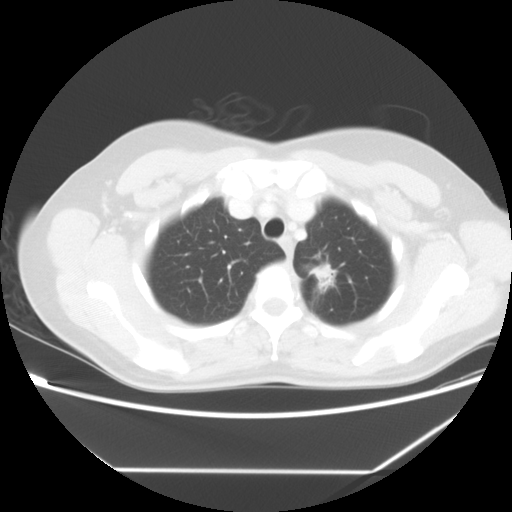
Chest CT, one axial slice. Position 49 of 60 along the scan axis. Reconstruction kernel STANDARD. Lung window (W 1500 / L -600 HU). 5 mm slice thickness. 512 × 512 image matrix. Patient: female, 43 years. Case-level facts recorded for this patient, not image findings: clinical TNM (as recorded): T1c N0 M1b.
Annotated regions visible in this slice (bounding box drawn by a radiologist):
- lung tumour (recorded histology: adenocarcinoma): bounding box <306,259,337,289> (left, top, right, bottom; pixels)